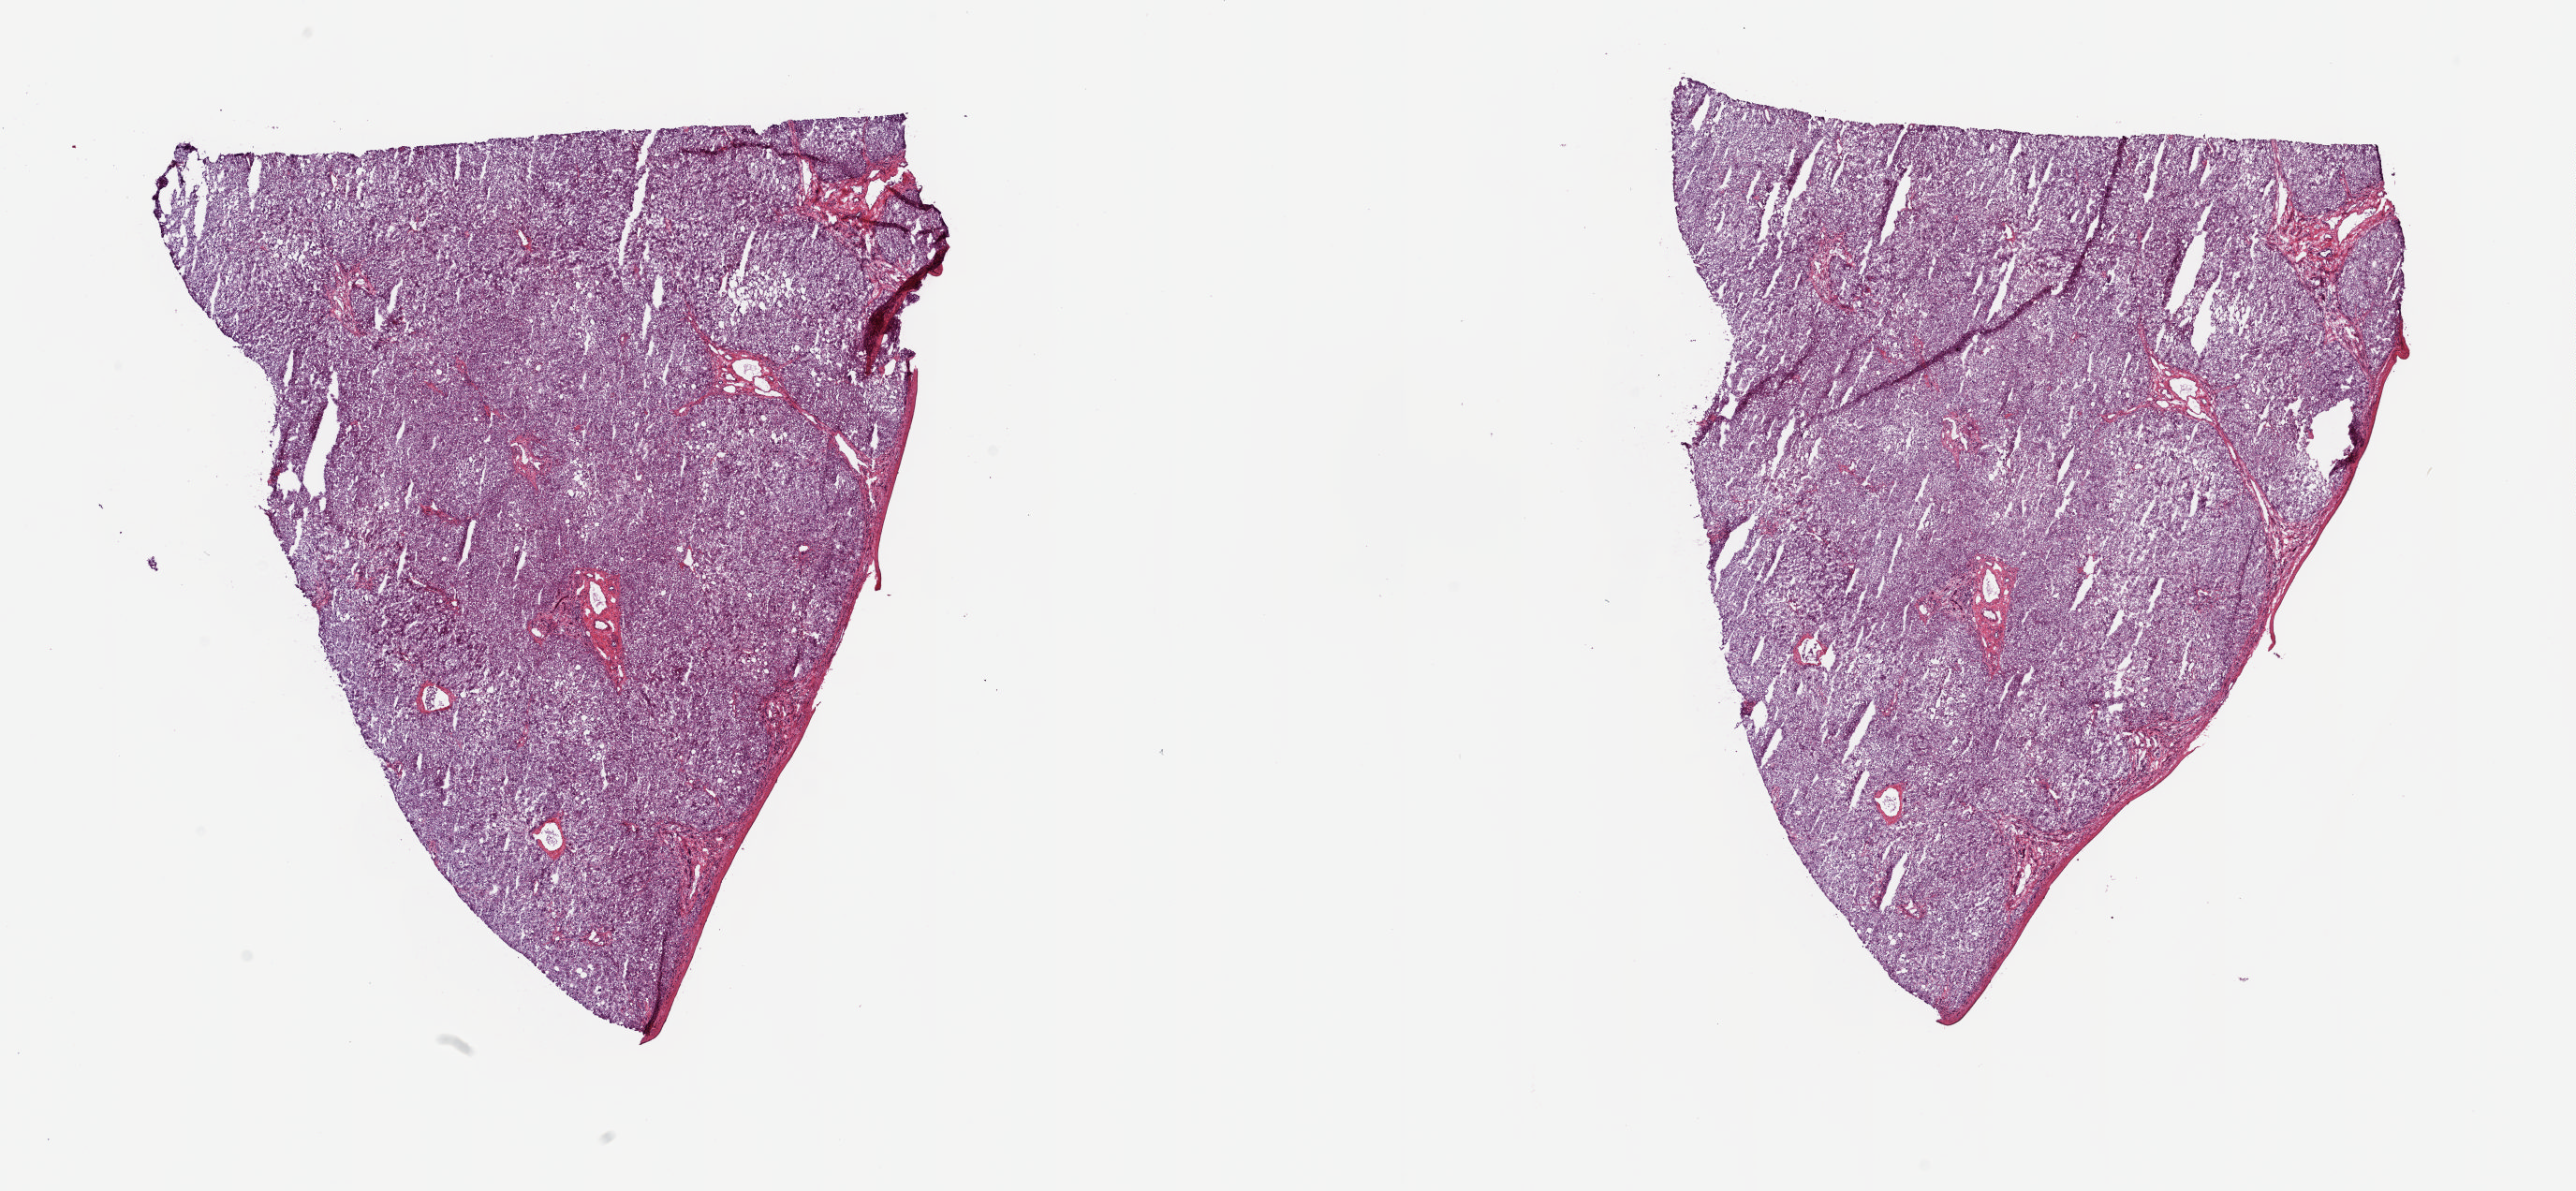
Digitized H&E-stained tissue section (whole slide), low-resolution overview of the scanned area, about 21.8 x 10.1 mm (acquisition: 20x scan). Frozen section from the top of the tissue portion. Sample: solid tissue normal (non-tumour tissue), bile duct. Male patient; age at initial diagnosis 66 years. Pathologist review of this section (percent, as recorded): tumour cells 0%, tumour nuclei 0%, normal cells 100%, stromal cells 0%, necrosis 0%. Inflammatory infiltration, as recorded: lymphocyte infiltration 2%, monocyte infiltration 0%, neutrophil infiltration 0%.
* this section: solid tissue normal (non-tumour) sample from the same patient
* patient diagnosis: Cholangiocarcinoma (intrahepatic bile duct)